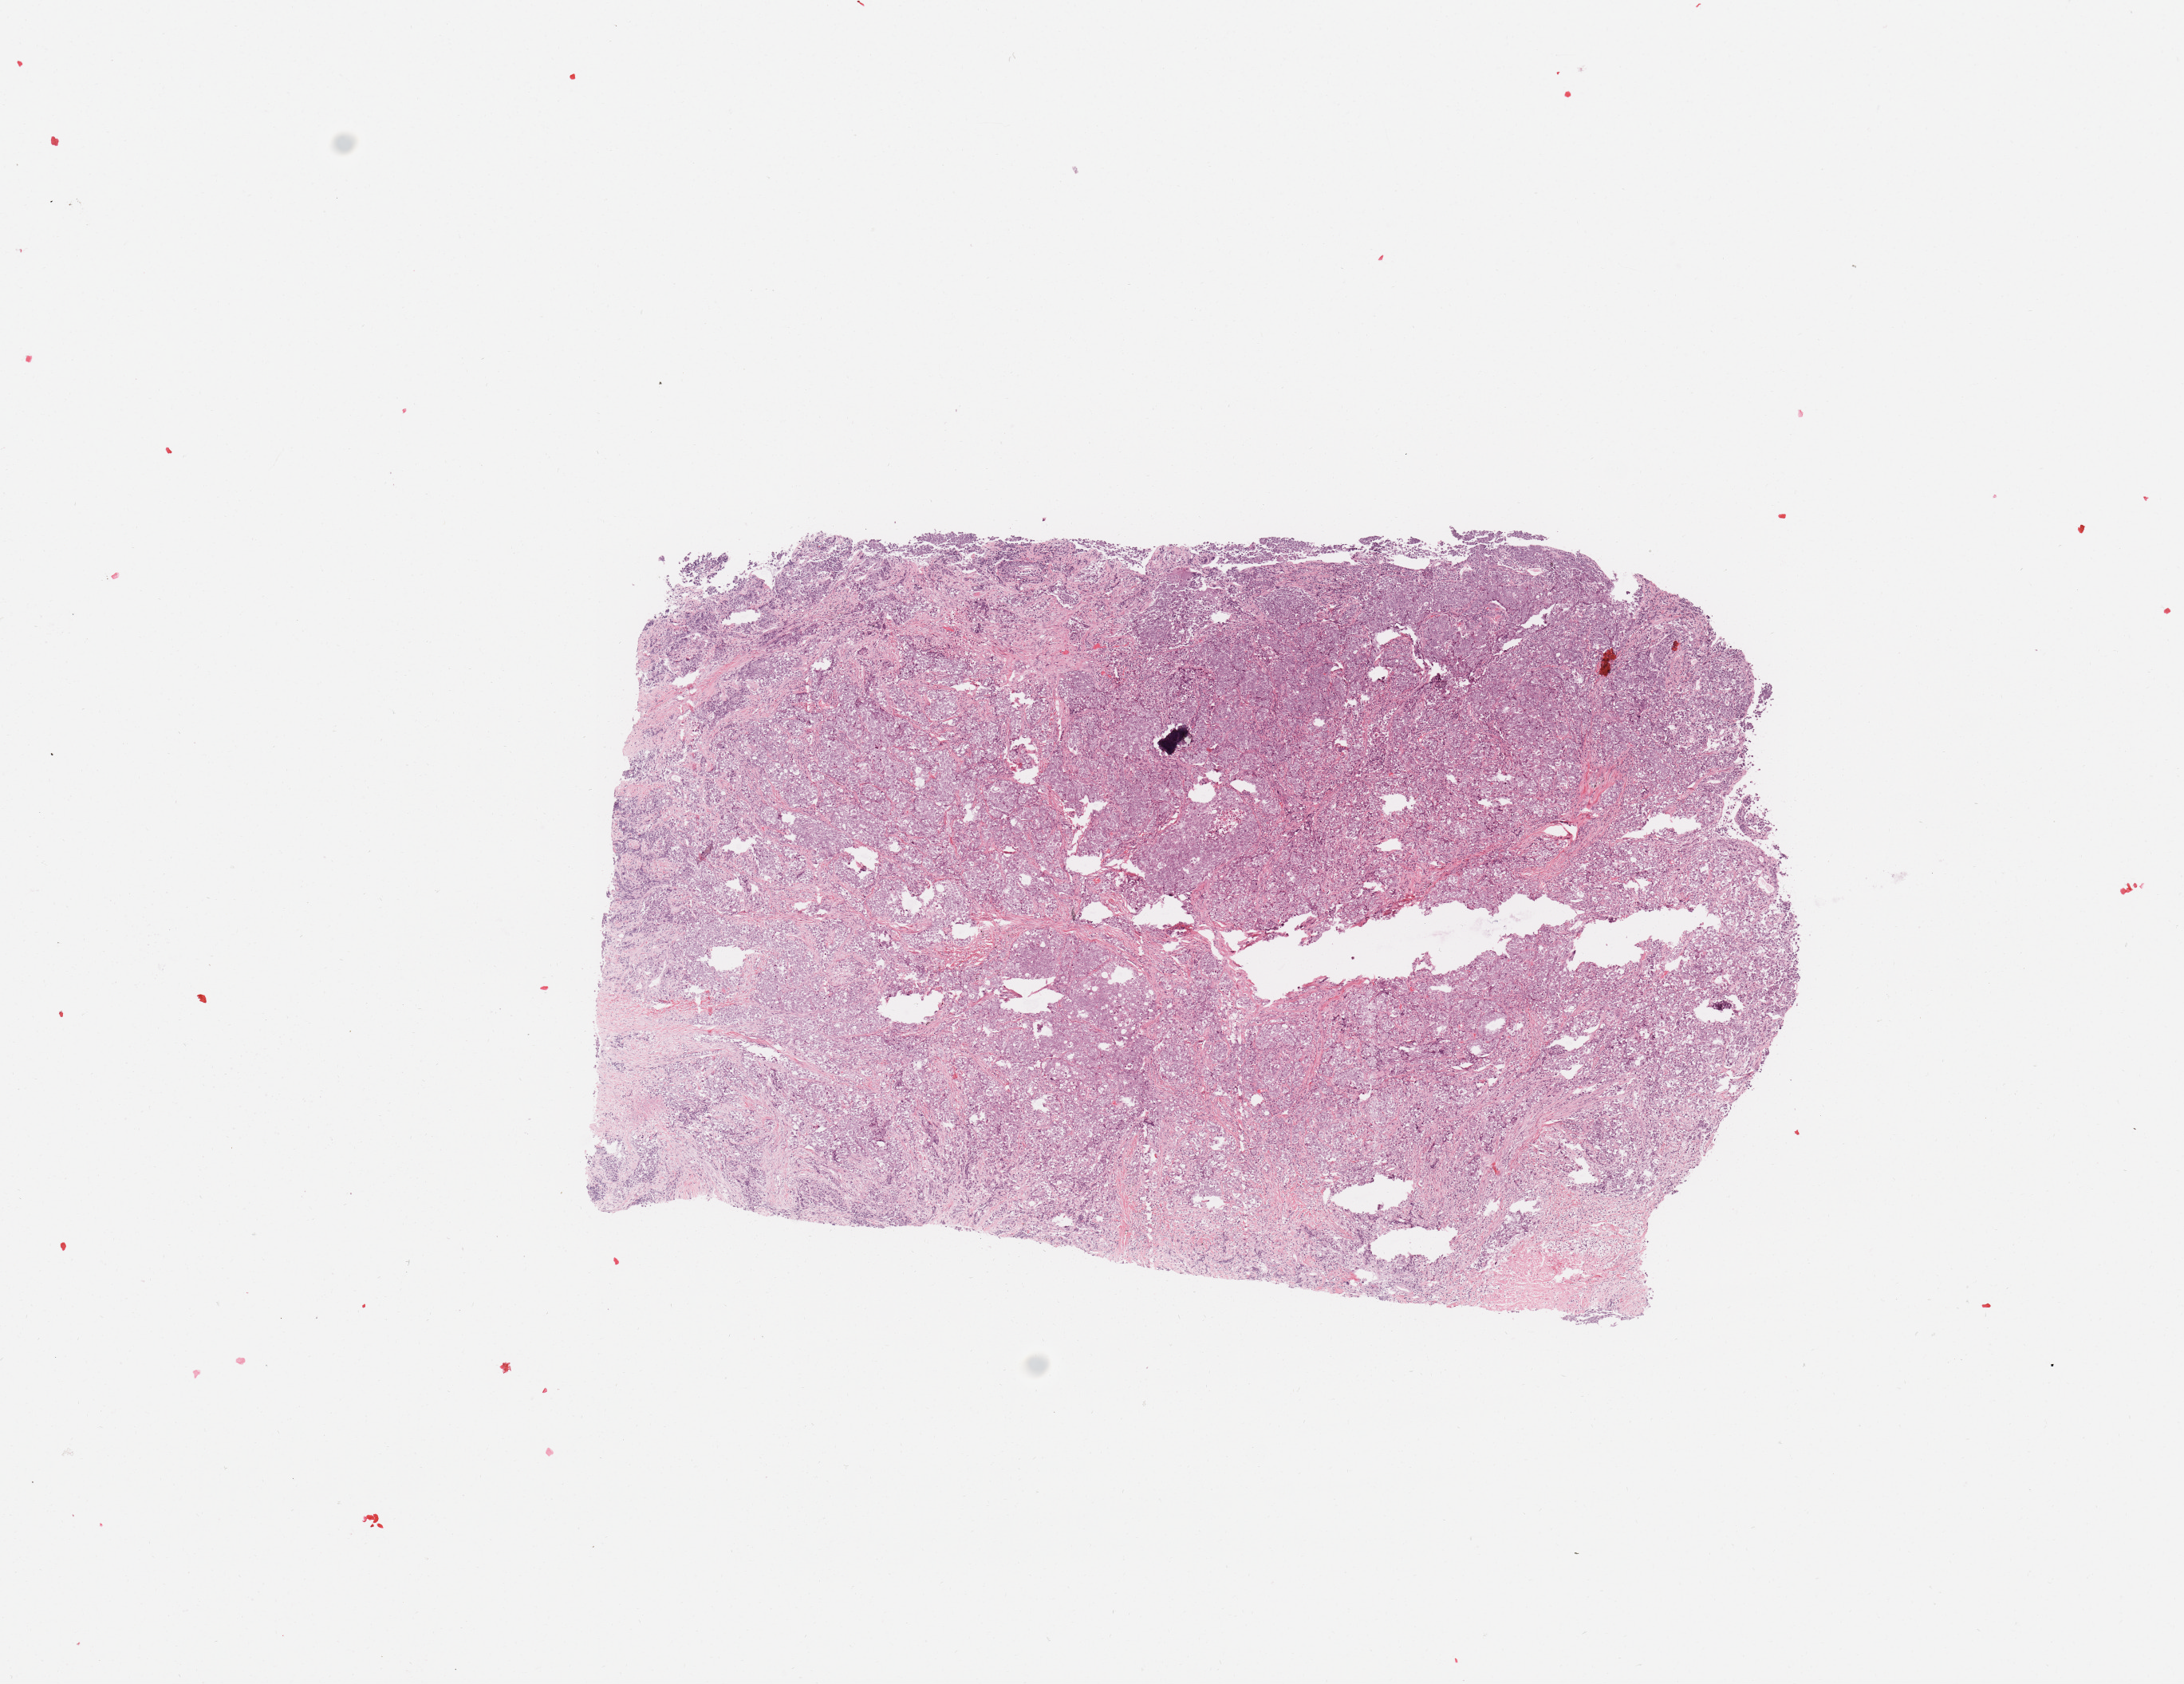
Whole-slide histology image, Hematoxylin and eosin (H&E) stained, a low-resolution overview of the entire scanned area, about 10.8 x 8.3 mm (acquisition: 20x scan). Tumour tissue sample, sampled site: lung. 44-year-old male patient. Histologic grade: G3 (poorly differentiated). Pathologist review of this section (percent, as recorded): tumour nuclei 90%, necrosis 2%.
Diagnosis: Squamous cell carcinoma, NOS. AJCC pathologic stage: IIB. Primary tumour site (as recorded): left upper lobe.